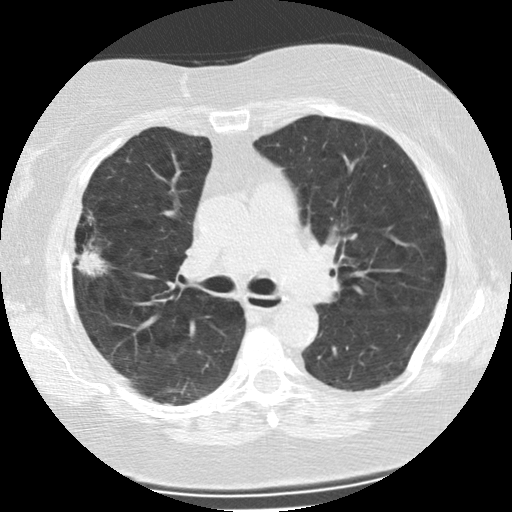
Low-dose screening chest CT, one axial slice. Position 143 of 225 along the scan axis. Reconstruction kernel STANDARD. 120 kVp. Lung window (W 1500 / L -600 HU). 512 × 512 image matrix.
Annotated regions visible in this slice (outlined manually by an expert reader):
- lesion 1 (tumor, upper lobe of right lung): bounding box <77,246,107,277> (left, top, right, bottom; pixels)